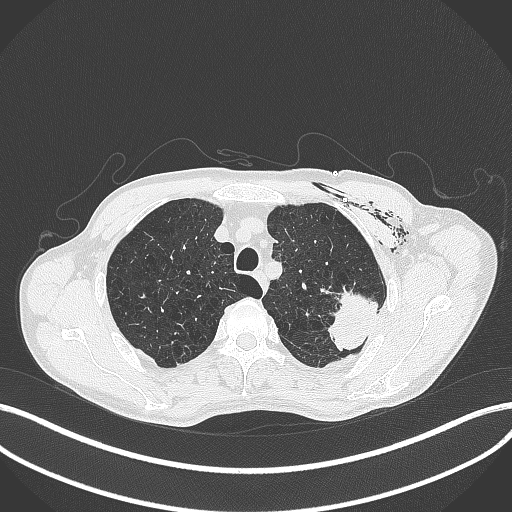
Chest CT, one axial slice; position 334 of 457 along the scan axis; reconstruction kernel B70f; 120 kVp; lung window (W 1500 / L -600 HU); 512 × 512 image matrix, field of view 400 × 400 mm. Patient: male, 58 years. From the clinical record (not read from this slice): clinical TNM (as recorded): T3 N0 M0.
Outlined on this slice (rectangle marked by the reading radiologist):
- lung tumour (recorded histology: adenocarcinoma): bounding box (x1, y1, x2, y2) in pixels: (319, 284, 379, 353)